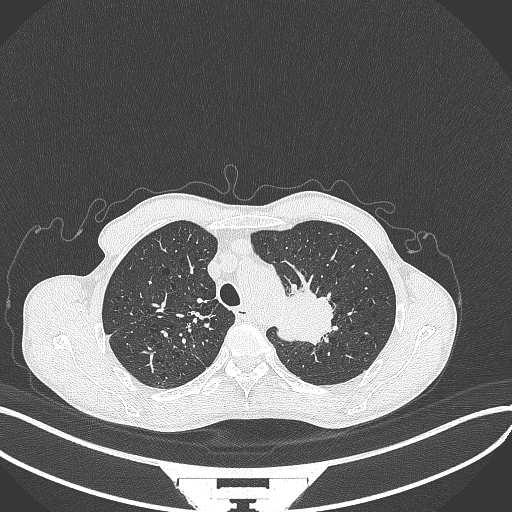
Chest CT, one axial slice; position 332 of 386 along the scan axis; reconstruction kernel B70f; lung window (W 1500 / L -600 HU); 1 mm slice thickness; 512 × 512 image matrix, field of view 400 × 400 mm. Male patient, age 65 years. Case-level facts recorded for this patient, not image findings: clinical TNM (as recorded): T2b N0 M0; histopathological grade: G2.
Outlined on this slice (bounding box drawn by a radiologist):
- lung tumour (recorded histology: adenocarcinoma): box from (x=274, y=282) to (x=334, y=347) px